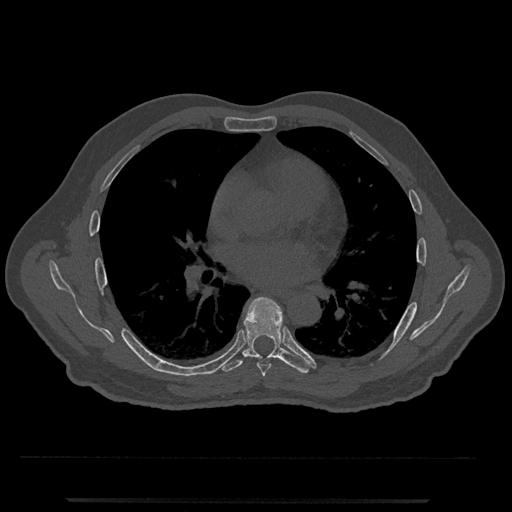
CT including the spine, one axial slice. Slice 706 of 797 in the series (ordered by position). Reconstruction kernel Br40s/3. 120 kVp. Bone window (W 1800 / L 400 HU). 0.5 mm slice thickness. 512 × 512 image matrix, field of view 419 × 419 mm. Patient: male, 63 years. Case-level facts recorded for this patient, not image findings: primary cancer: prostate.
Outlined on this slice (semi-automatic segmentation, software-assisted and operator-edited):
- T6 vertebra: bounding box <257,363,271,377> (left, top, right, bottom; pixels)
- T7 vertebra: <219,296,310,374>